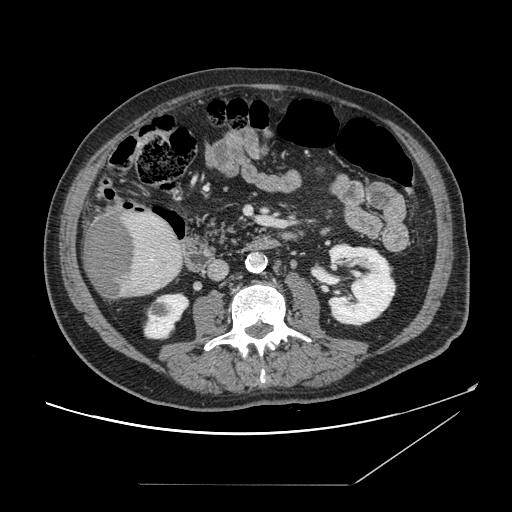
Contrast-enhanced abdominal CT, one axial slice; slice 45 of 166 in the series (ordered by position); intravenous contrast given; soft-tissue window (W 400 / L 40 HU); 512 × 512 image matrix, field of view 416 × 416 mm. Male patient, age 80 years. Case-level facts recorded for this patient, not image findings: diagnosis: colorectal cancer liver metastases, imaged before liver resection; multiple liver metastases: no; largest metastasis: 2.2 cm.
Structures marked on this image (expert manual segmentation):
- liver: bounding box (x1, y1, x2, y2) in pixels: (84, 208, 184, 300)
- liver metastasis: (83, 215, 136, 298)